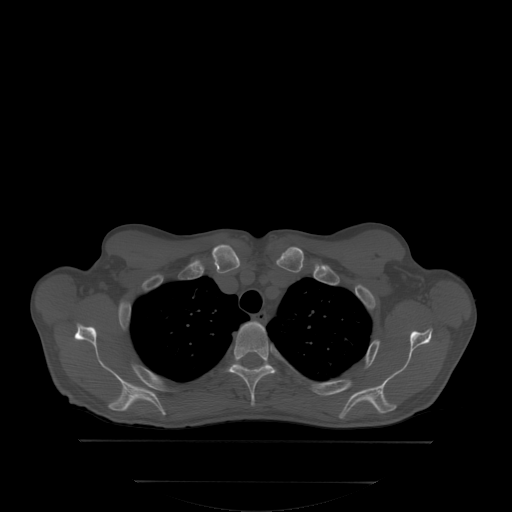
CT including the spine, one axial slice. Bone window (W 1800 / L 400 HU). 2.5 mm slice thickness. 512 × 512 image matrix. Male patient, age 58 years. Case-level facts recorded for this patient, not image findings: primary cancer: prostate; vertebrae with lytic lesions (as recorded): L1.
Outlined on this slice (semi-automatically segmented with operator editing):
- T3 vertebra: bounding box (x1, y1, x2, y2) in pixels: (226, 322, 276, 403)